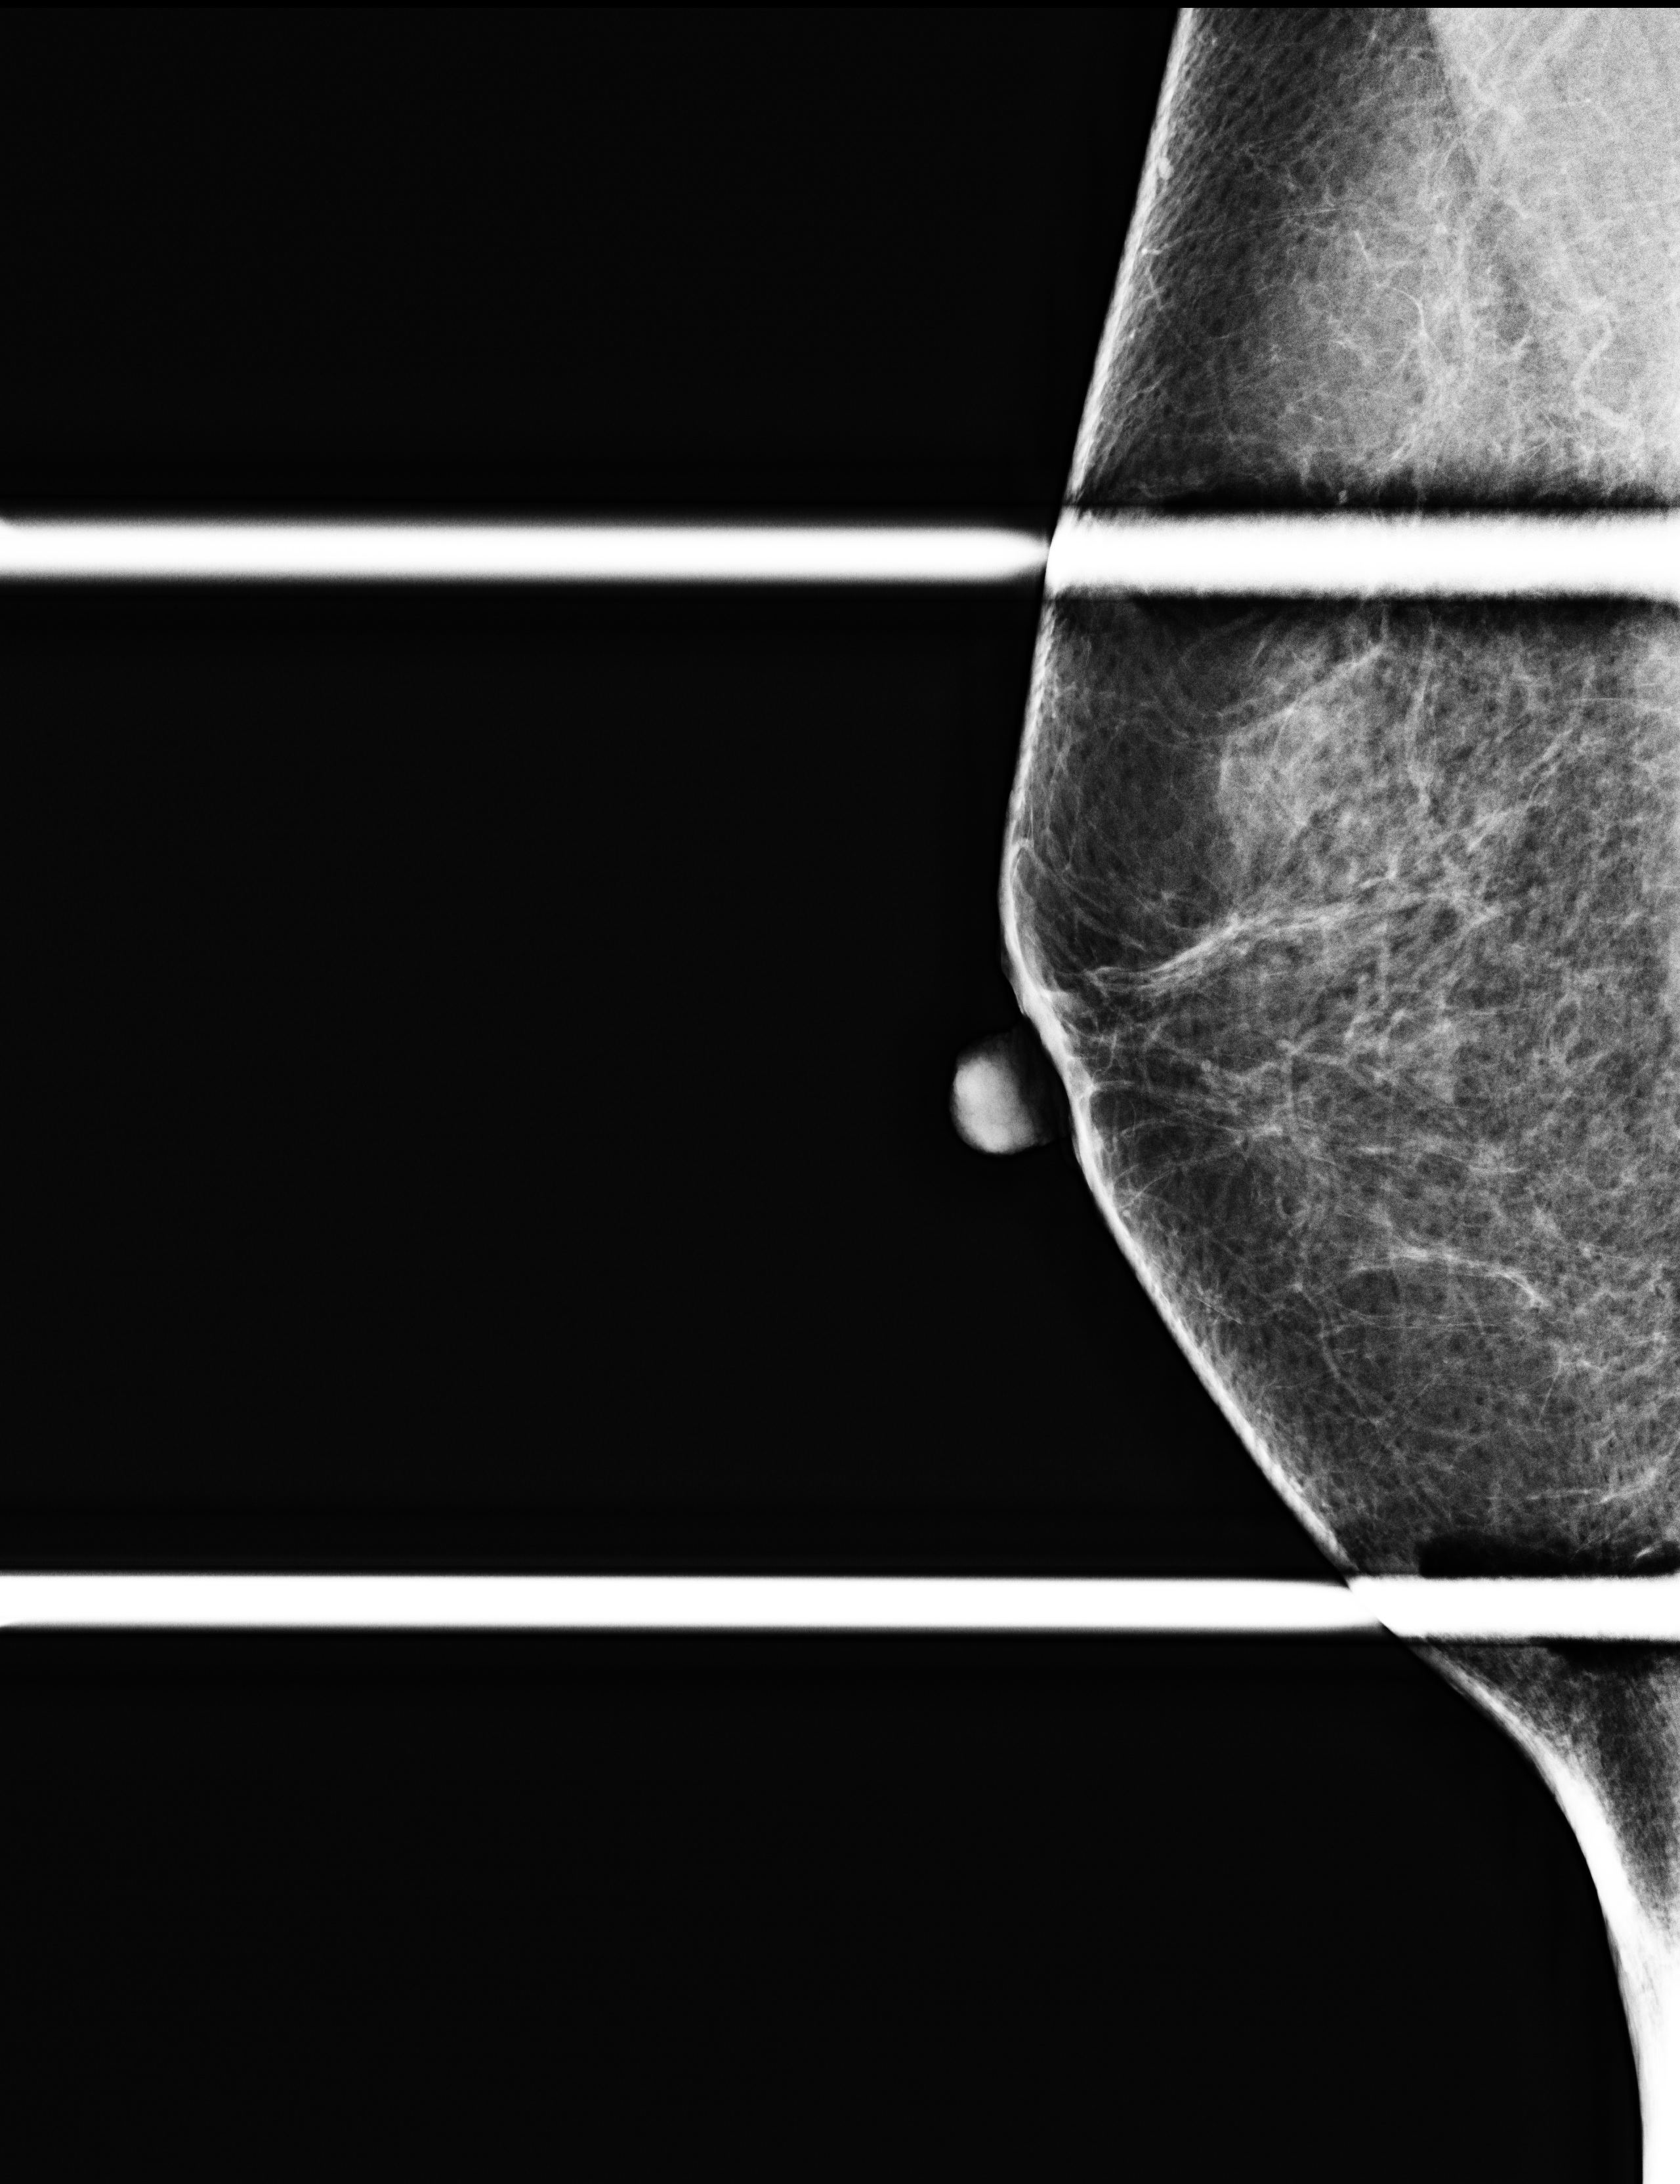
Full-field digital mammogram (FFDM); right breast; ML view (spot compression); additional (diagnostic) view. Patient aged 61 years (female).
Breast density at the screening exam (both breasts): heterogeneously dense (BI-RADS density category c). Final BI-RADS category for the screening round (tomosynthesis exam, both breasts): category 2. Recall: recalled for additional imaging after this screen.